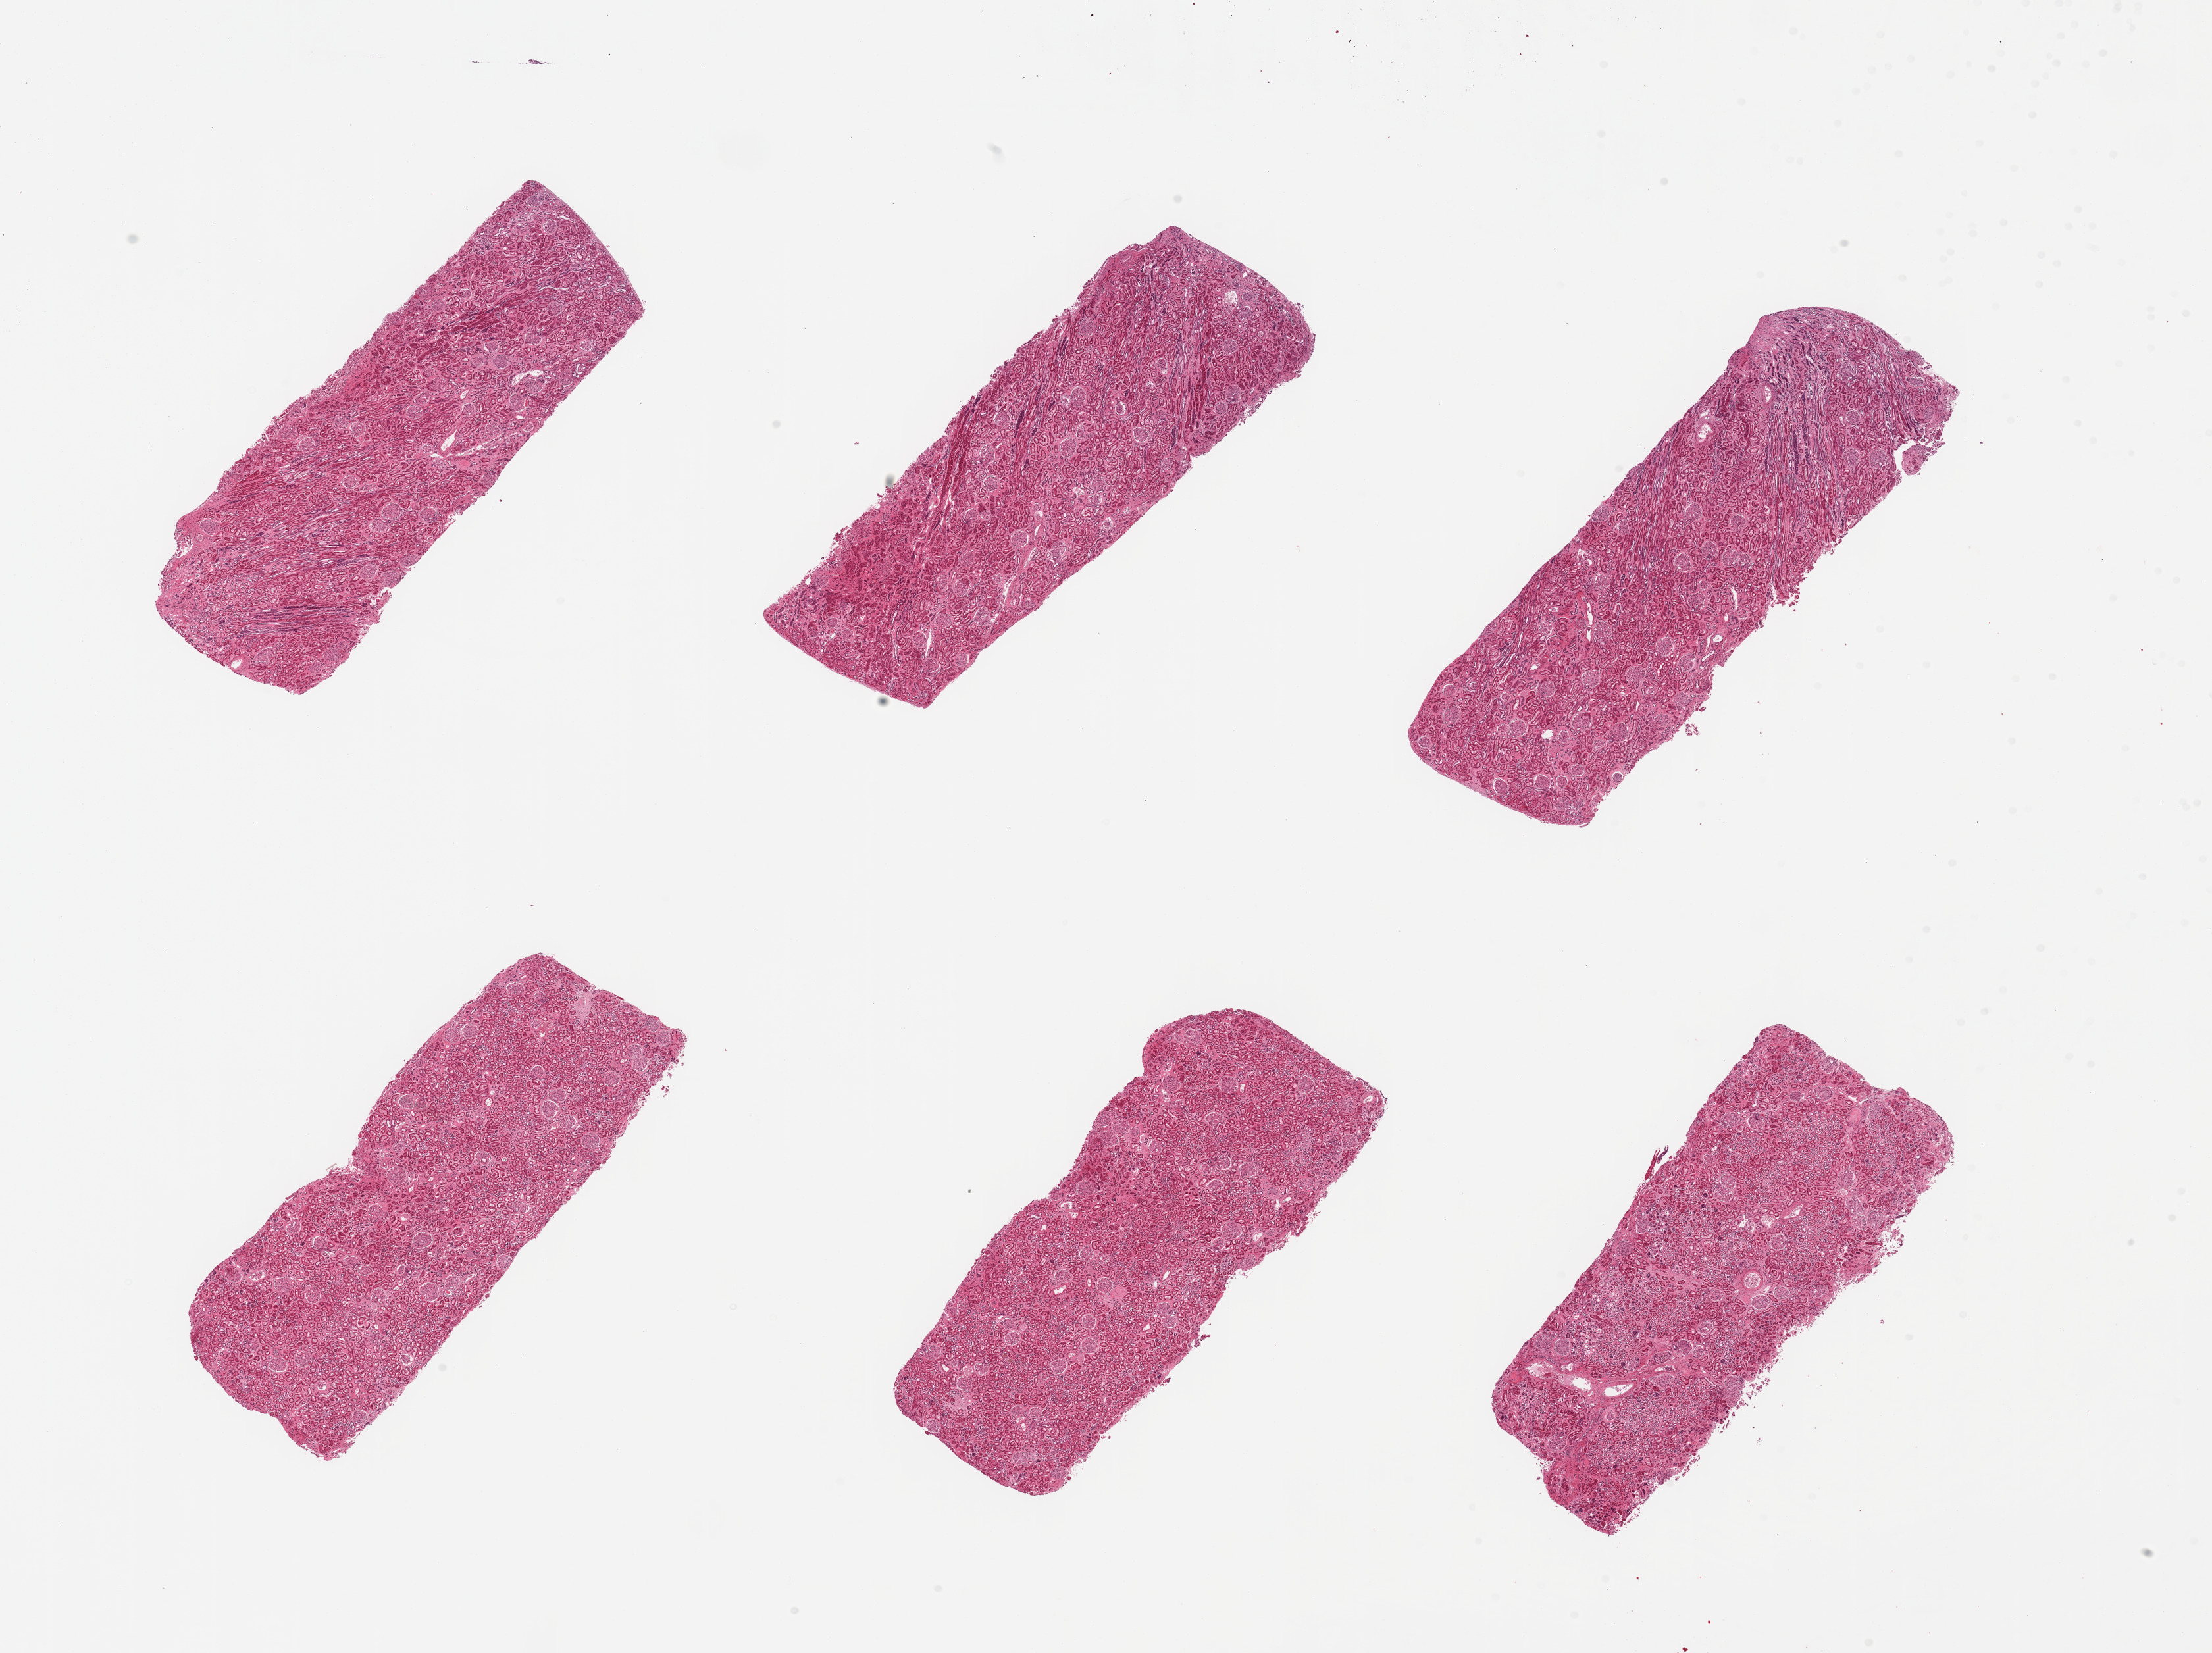
Haematoxylin and eosin whole-slide image, shown as a low-resolution overview of the whole scanned area (about 26.6 x 19.9 mm, acquisition: 20x scan), PAXgene-fixed paraffin-embedded (PFPE) section, section of renal cortex (target tissue), tissue donor sample. Donor: female.
Reviewer comment on this tissue sample: 2 pieces; no active or chronic lesions; tubules moderately autolyzed.